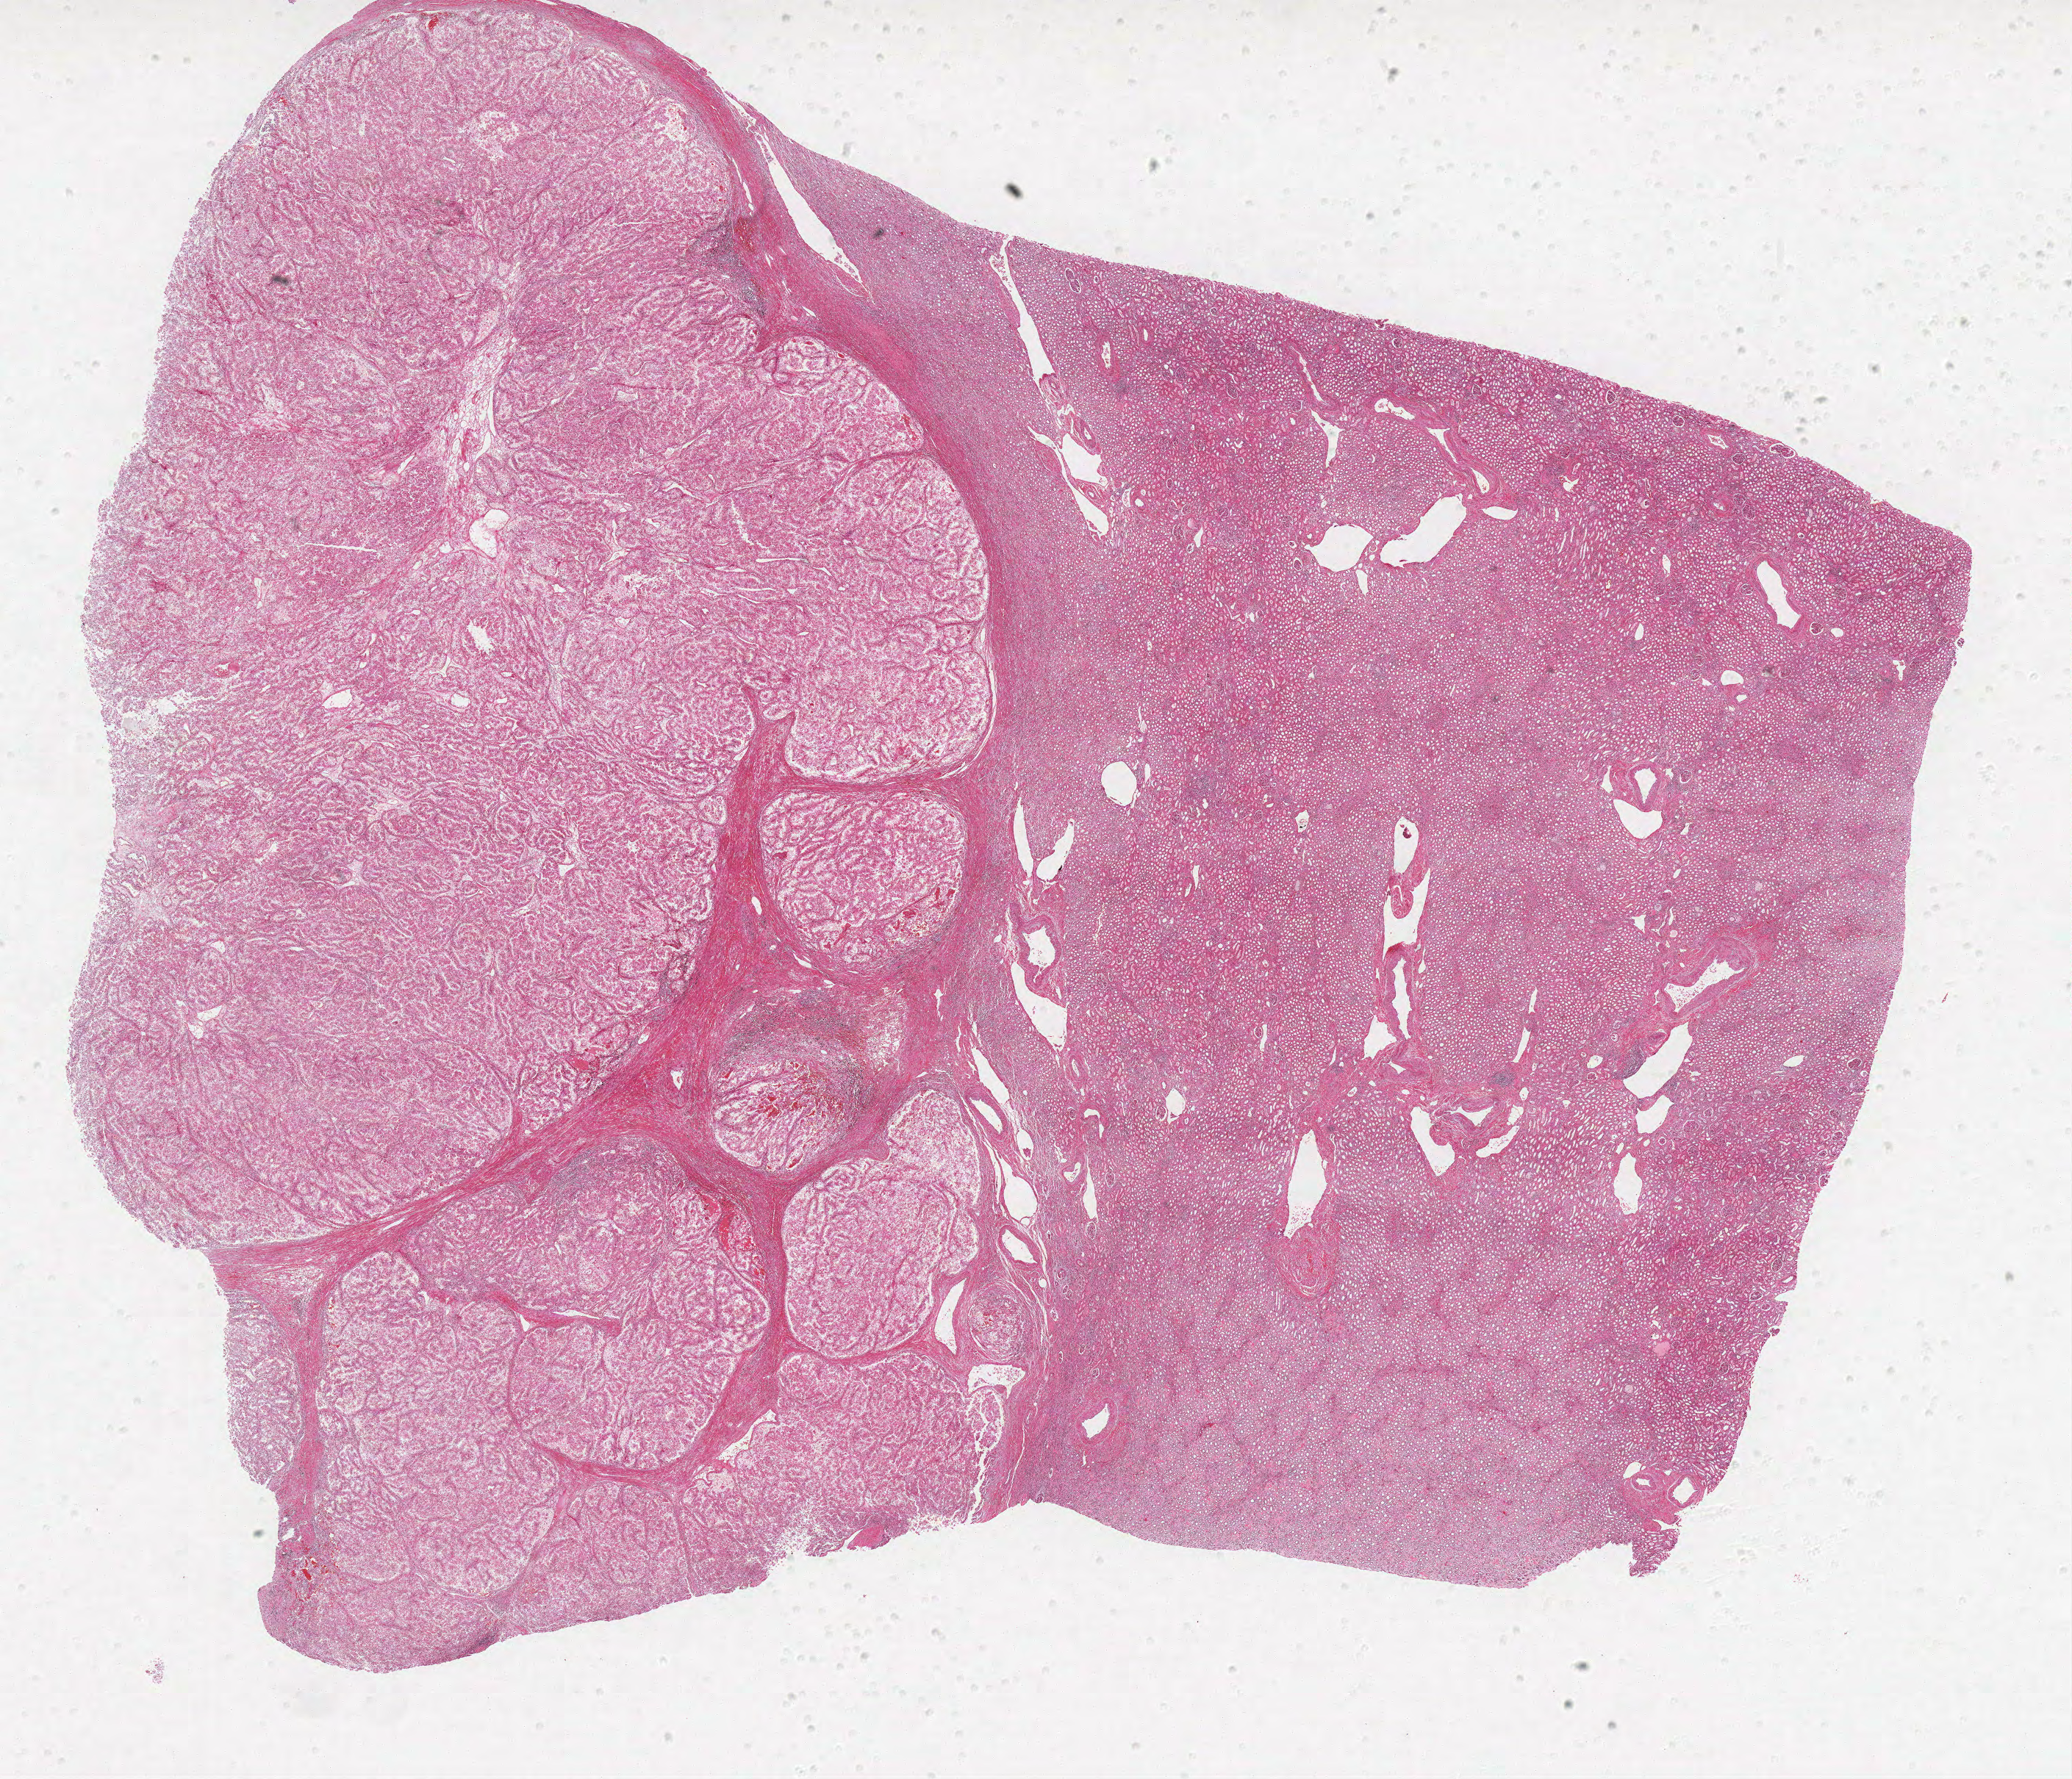
Whole-slide histology image, H&E, low-resolution overview of the scanned area, about 22.5 x 19.4 mm. Formalin-fixed paraffin-embedded (FFPE) diagnostic section. Kidney, primary tumour sample. Male patient; age at initial diagnosis 58 years.
Histologic diagnosis: Clear cell adenocarcinoma, NOS.